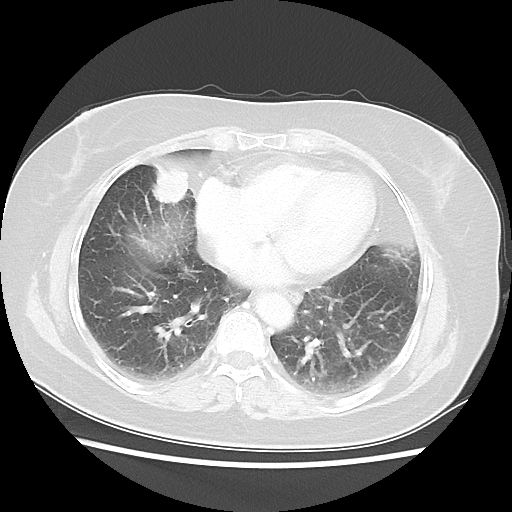
Chest CT, one axial slice. 100 kVp. Lung window (W 1500 / L -600 HU). 5 mm slice thickness. 512 × 512 image matrix. Patient: female, 61 years. Case-level facts recorded for this patient, not image findings: clinical TNM (as recorded): T1c N0 M0.
Annotated regions visible in this slice (rectangle marked by the reading radiologist):
- lung tumour (recorded histology: adenocarcinoma): bounding box <146,161,190,203> (left, top, right, bottom; pixels)